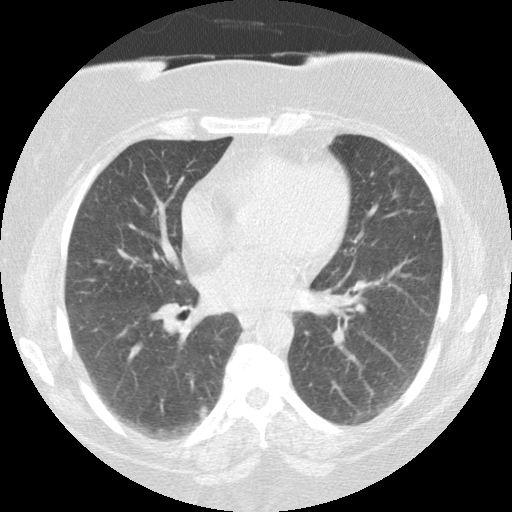
Low-dose screening chest CT, axial slice. Baseline annual screen. Lung window (W 1500 / L -600 HU). Standard (soft-tissue) reconstruction kernel (STANDARD). Female participant, aged 58 years at enrolment.
- Expert-annotated lung lesion, bounding box (x1, y1, x2, y2) in pixels: (177, 390, 228, 441).
- The screening reader recorded 4 non-calcified nodules or masses ≥4 mm on this exam (left lower lobe, lingula, right middle lobe, right upper lobe); which of them this box marks is not recorded.
- Official screen result: positive, change unspecified: nodule(s) >= 4 mm or enlarging nodule(s), mass(es), or other non-specific abnormalities suspicious for lung cancer.